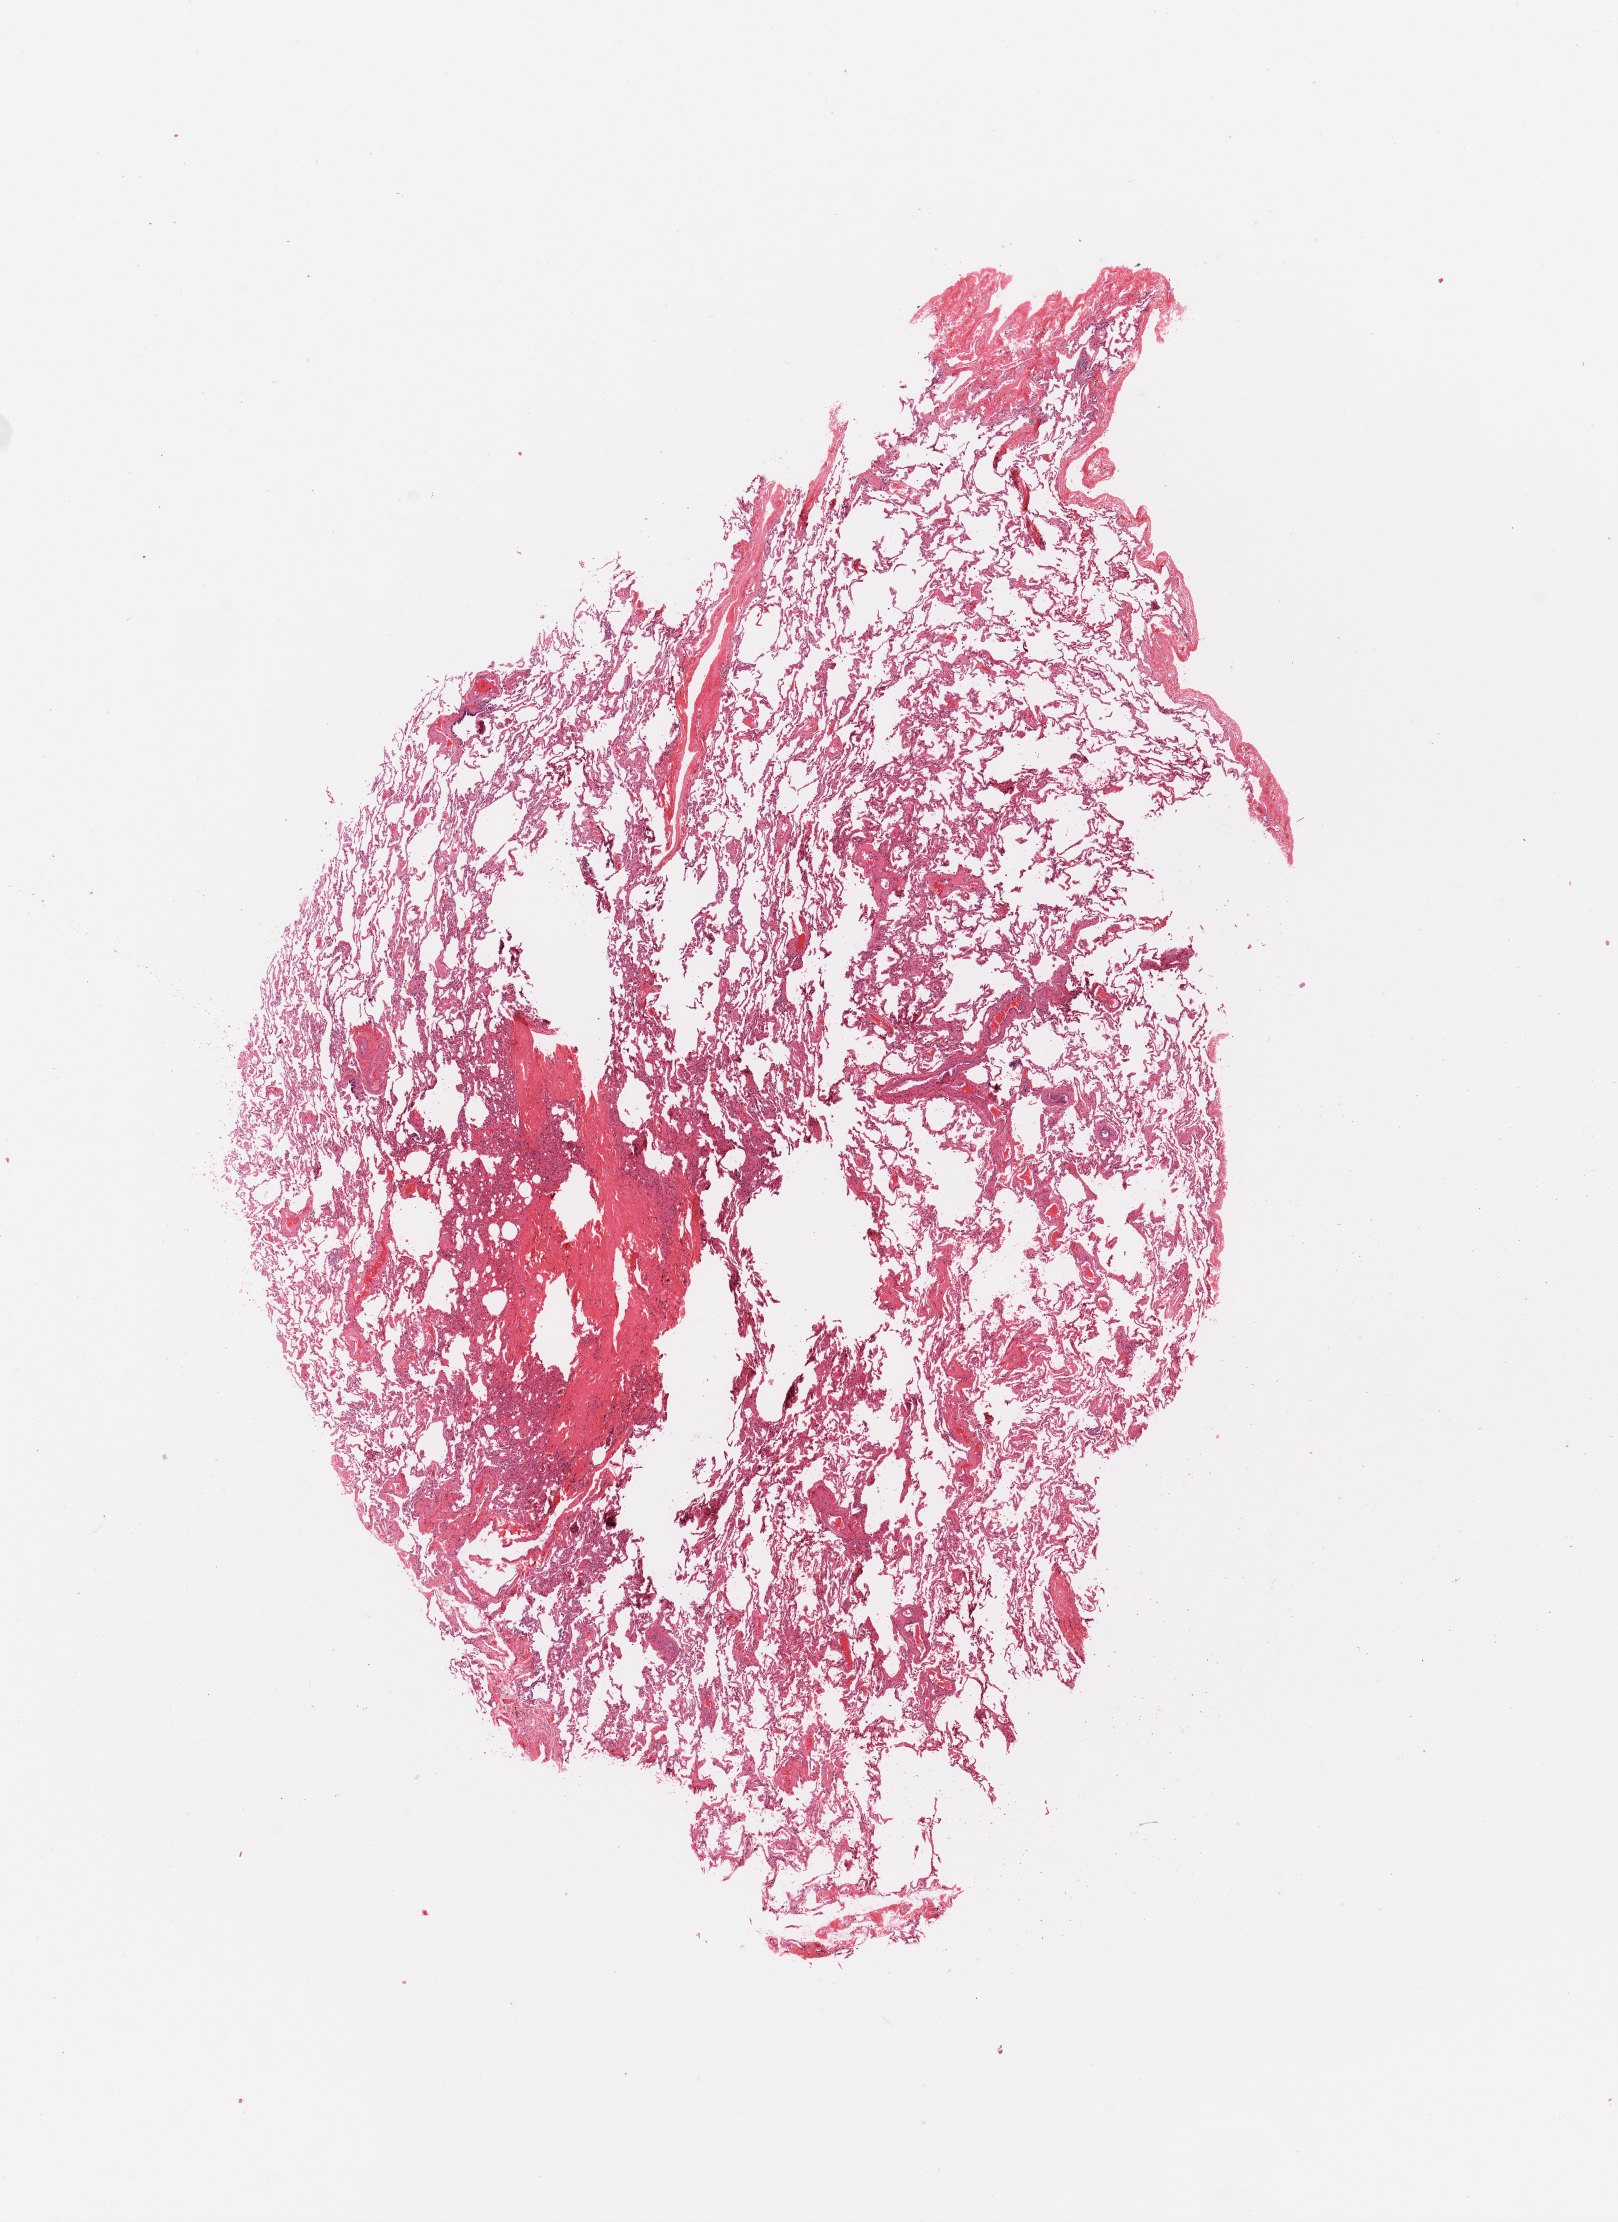
Whole-slide histology image, H&E, whole scanned area (about 12.8 x 17.6 mm) shown as a low-resolution overview. Normal (non-tumour) tissue sample, sampled site: lung. Female, 57 y/o.
This section: normal (non-tumour) tissue from the same patient. Patient diagnosis: Adenocarcinoma, NOS.